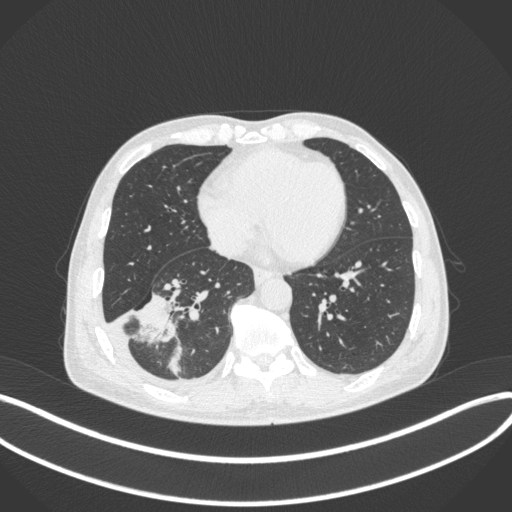
Chest CT, one axial slice. Position 136 of 385 along the scan axis. Reconstruction kernel B31f. Lung window (W 1500 / L -600 HU). 1 mm slice thickness. 512 × 512 image matrix. Male patient, age 64 years. From the clinical record (not read from this slice): clinical TNM (as recorded): T3 N0 M0; histopathological grade: G2-3.
Outlined on this slice (rectangle marked by the reading radiologist):
- lung tumour (recorded histology: adenocarcinoma): bounding box <130,289,182,345> (left, top, right, bottom; pixels)